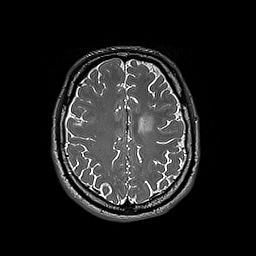
Brain MRI from a brain-tumour surgery series, one axial slice. Slice 63 of 192 in the series (ordered by position). 256 × 256 image matrix, field of view 250 × 250 mm. Case-level facts recorded for this patient, not image findings: histopathology: Oligodendroglioma; WHO grade: 3; IDH mutation: yes.
Annotated regions visible in this slice (manually delineated by an expert):
- tumour: box from (x=138, y=116) to (x=154, y=132) px